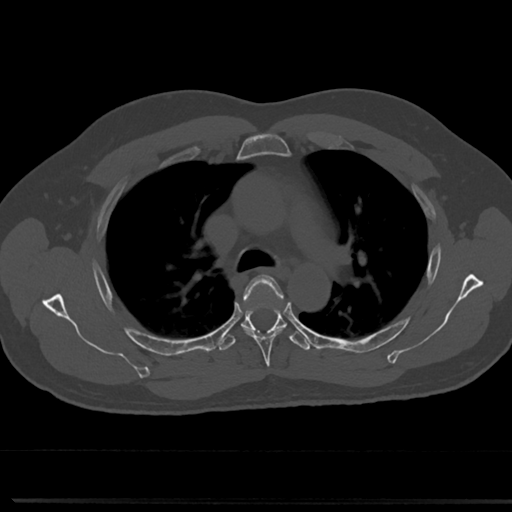
CT including the spine, one axial slice. Slice 524 of 817 in the series (ordered by position). Bone window (W 1800 / L 400 HU). 512 × 512 image matrix, field of view 355 × 355 mm. Patient: male, 61 years. Case-level facts recorded for this patient, not image findings: primary cancer: prostate.
Structures marked on this image (semi-automatically segmented with operator editing):
- T4 vertebra: bounding box [x1, y1, x2, y2] px = [238, 276, 288, 359]
- T5 vertebra: [241, 319, 308, 347]